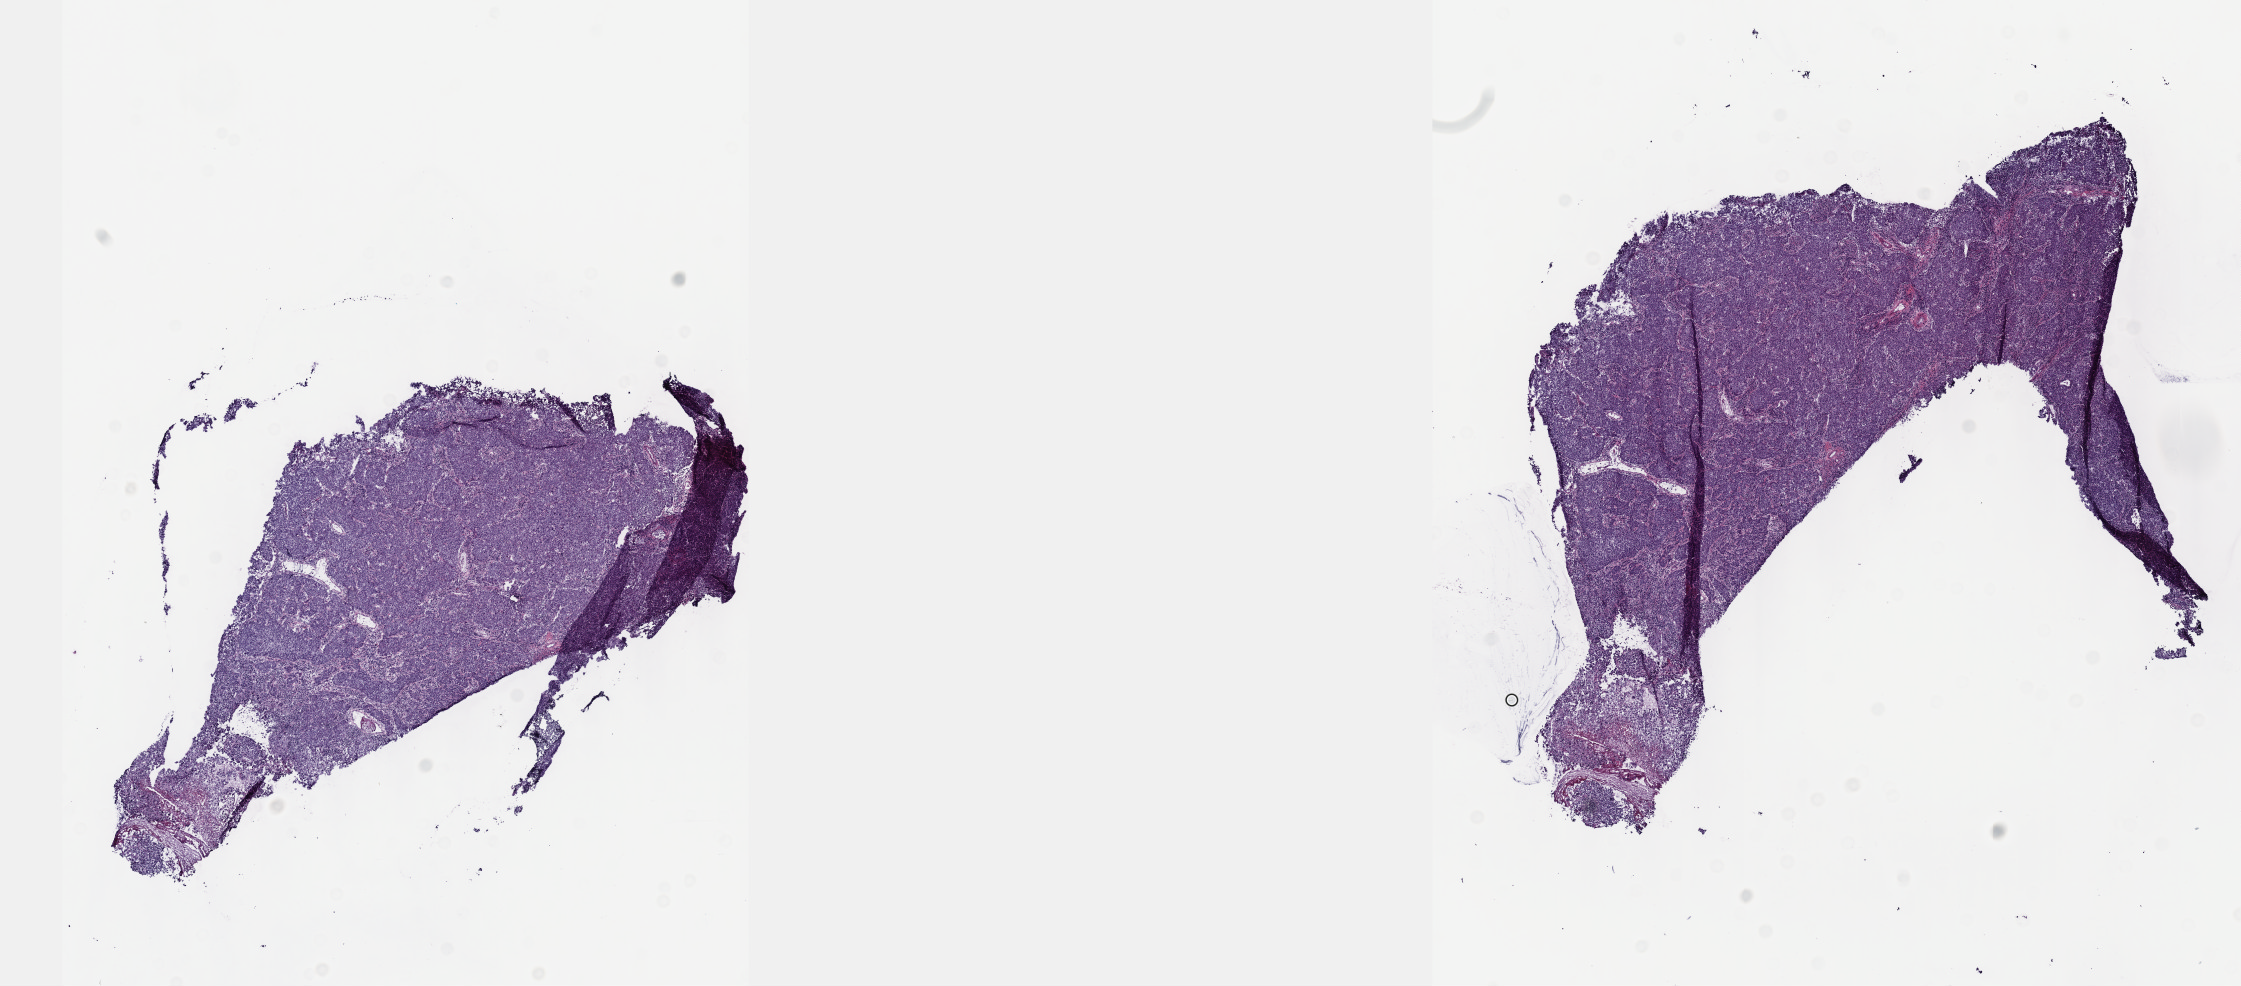
H&E whole-slide image — whole scanned area (about 18.1 x 8.0 mm, acquisition: 40x scan) shown as a low-resolution overview; frozen section from the top of the tissue portion; cervix, primary tumour sample. Female patient; age at initial diagnosis 44 years. Histologic grade: G3 (poorly differentiated). Slide review estimates, as recorded: tumour cells 80%, tumour nuclei 80%, normal cells 0%, stromal cells 20%, necrosis 0%. Inflammatory infiltration, as recorded: lymphocyte infiltration 10%, monocyte infiltration 0%, neutrophil infiltration 0%.
Lymph nodes positive (case pathology): 0 of 37 examined. Pathologic diagnosis: Squamous cell carcinoma, NOS. FIGO stage: IB1.